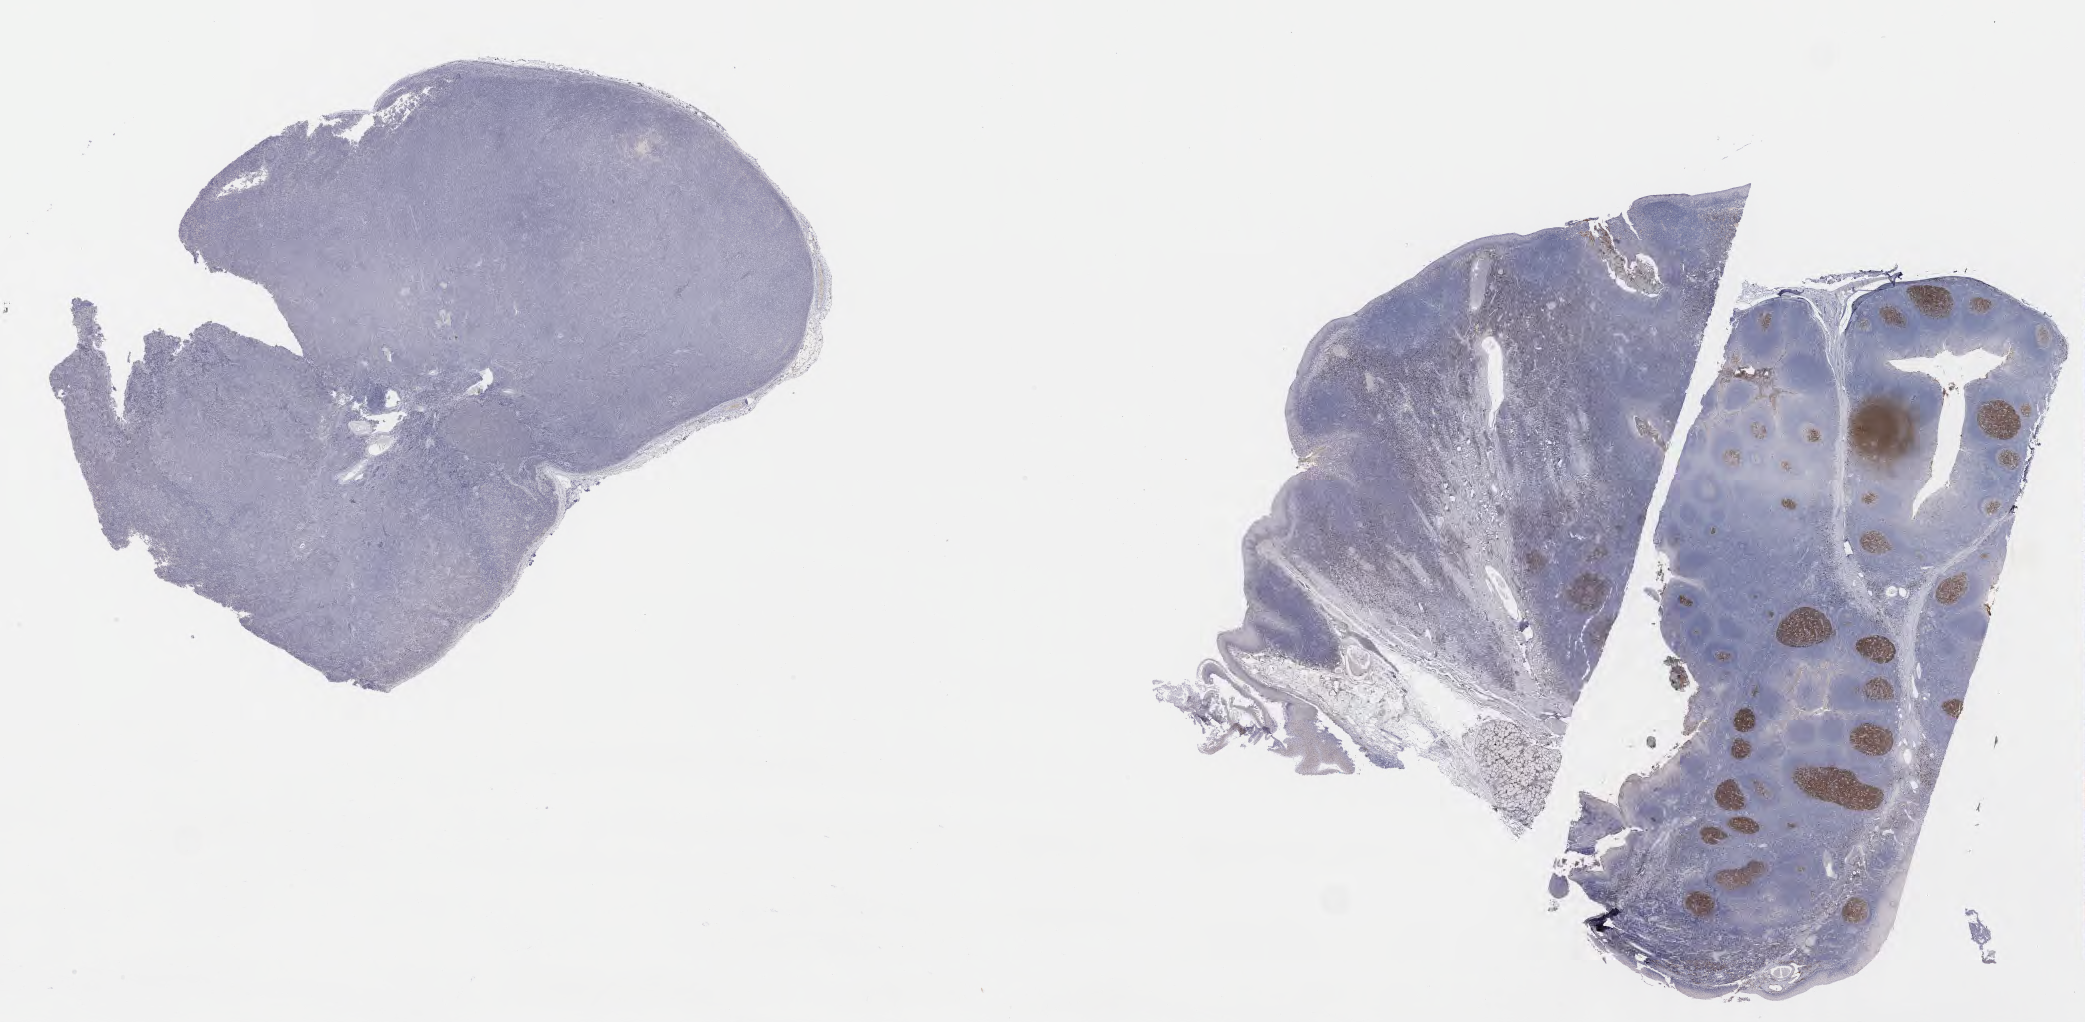
Immunohistochemistry (IHC) whole-slide image stained for CD10 — shown as a low-resolution overview of the whole scanned area (about 33.7 x 16.5 mm). Specimen: tumor tissue. Site: lymph node. Male patient, aged 32.
Diagnosis: Diffuse large B-cell lymphoma, NOS.